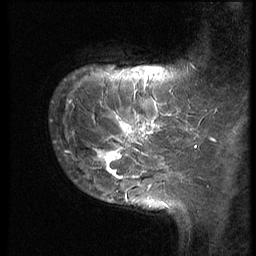
Breast MRI (dynamic contrast-enhanced), one sagittal slice. Position 9 of 62 along the scan axis. 3 images stored at this slice position (order not interpretable as contrast timing). 1.5 T. TE 4.2 ms, TR 9 ms. 2.5 mm slice thickness. 256 × 256 image matrix, field of view 180 × 180 mm. Female patient, age 28 years. From the clinical record (not read from this slice): setting: breast cancer imaged before/during neoadjuvant chemotherapy.
Structures marked on this image (semi-automatically segmented with operator editing):
- analysis volume of interest (the breast-tissue region the enhancement analysis was run in; not a lesion): bounding box (x1, y1, x2, y2) in pixels: (49, 82, 192, 184)
- tumour enhancement mask (voxels above the 140 % enhancement threshold inside the analysis volume of interest): (64, 90, 192, 179)